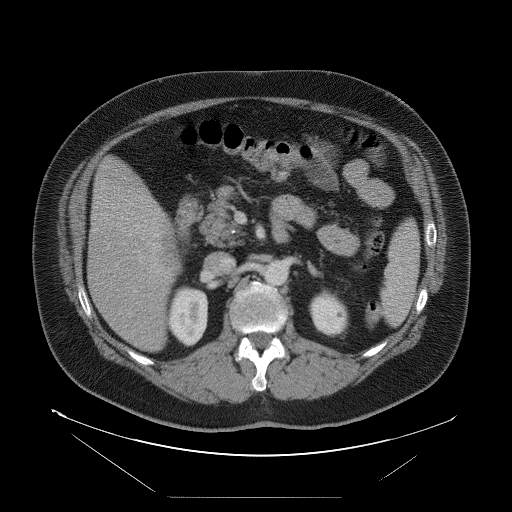
Contrast-enhanced abdominal CT, one axial slice. Position 43 of 114 along the scan axis. 120 kVp. Intravenous contrast given. Soft-tissue window (W 400 / L 40 HU). 512 × 512 image matrix, field of view 500 × 500 mm. Male patient, age 61 years. From the clinical record (not read from this slice): diagnosis: colorectal cancer liver metastases, imaged before liver resection; multiple liver metastases: no; largest metastasis: 6.5 cm.
Annotated regions visible in this slice (expert manual segmentation):
- liver: bounding box (x1, y1, x2, y2) in pixels: (89, 158, 180, 352)
- liver metastasis: (163, 233, 177, 265)